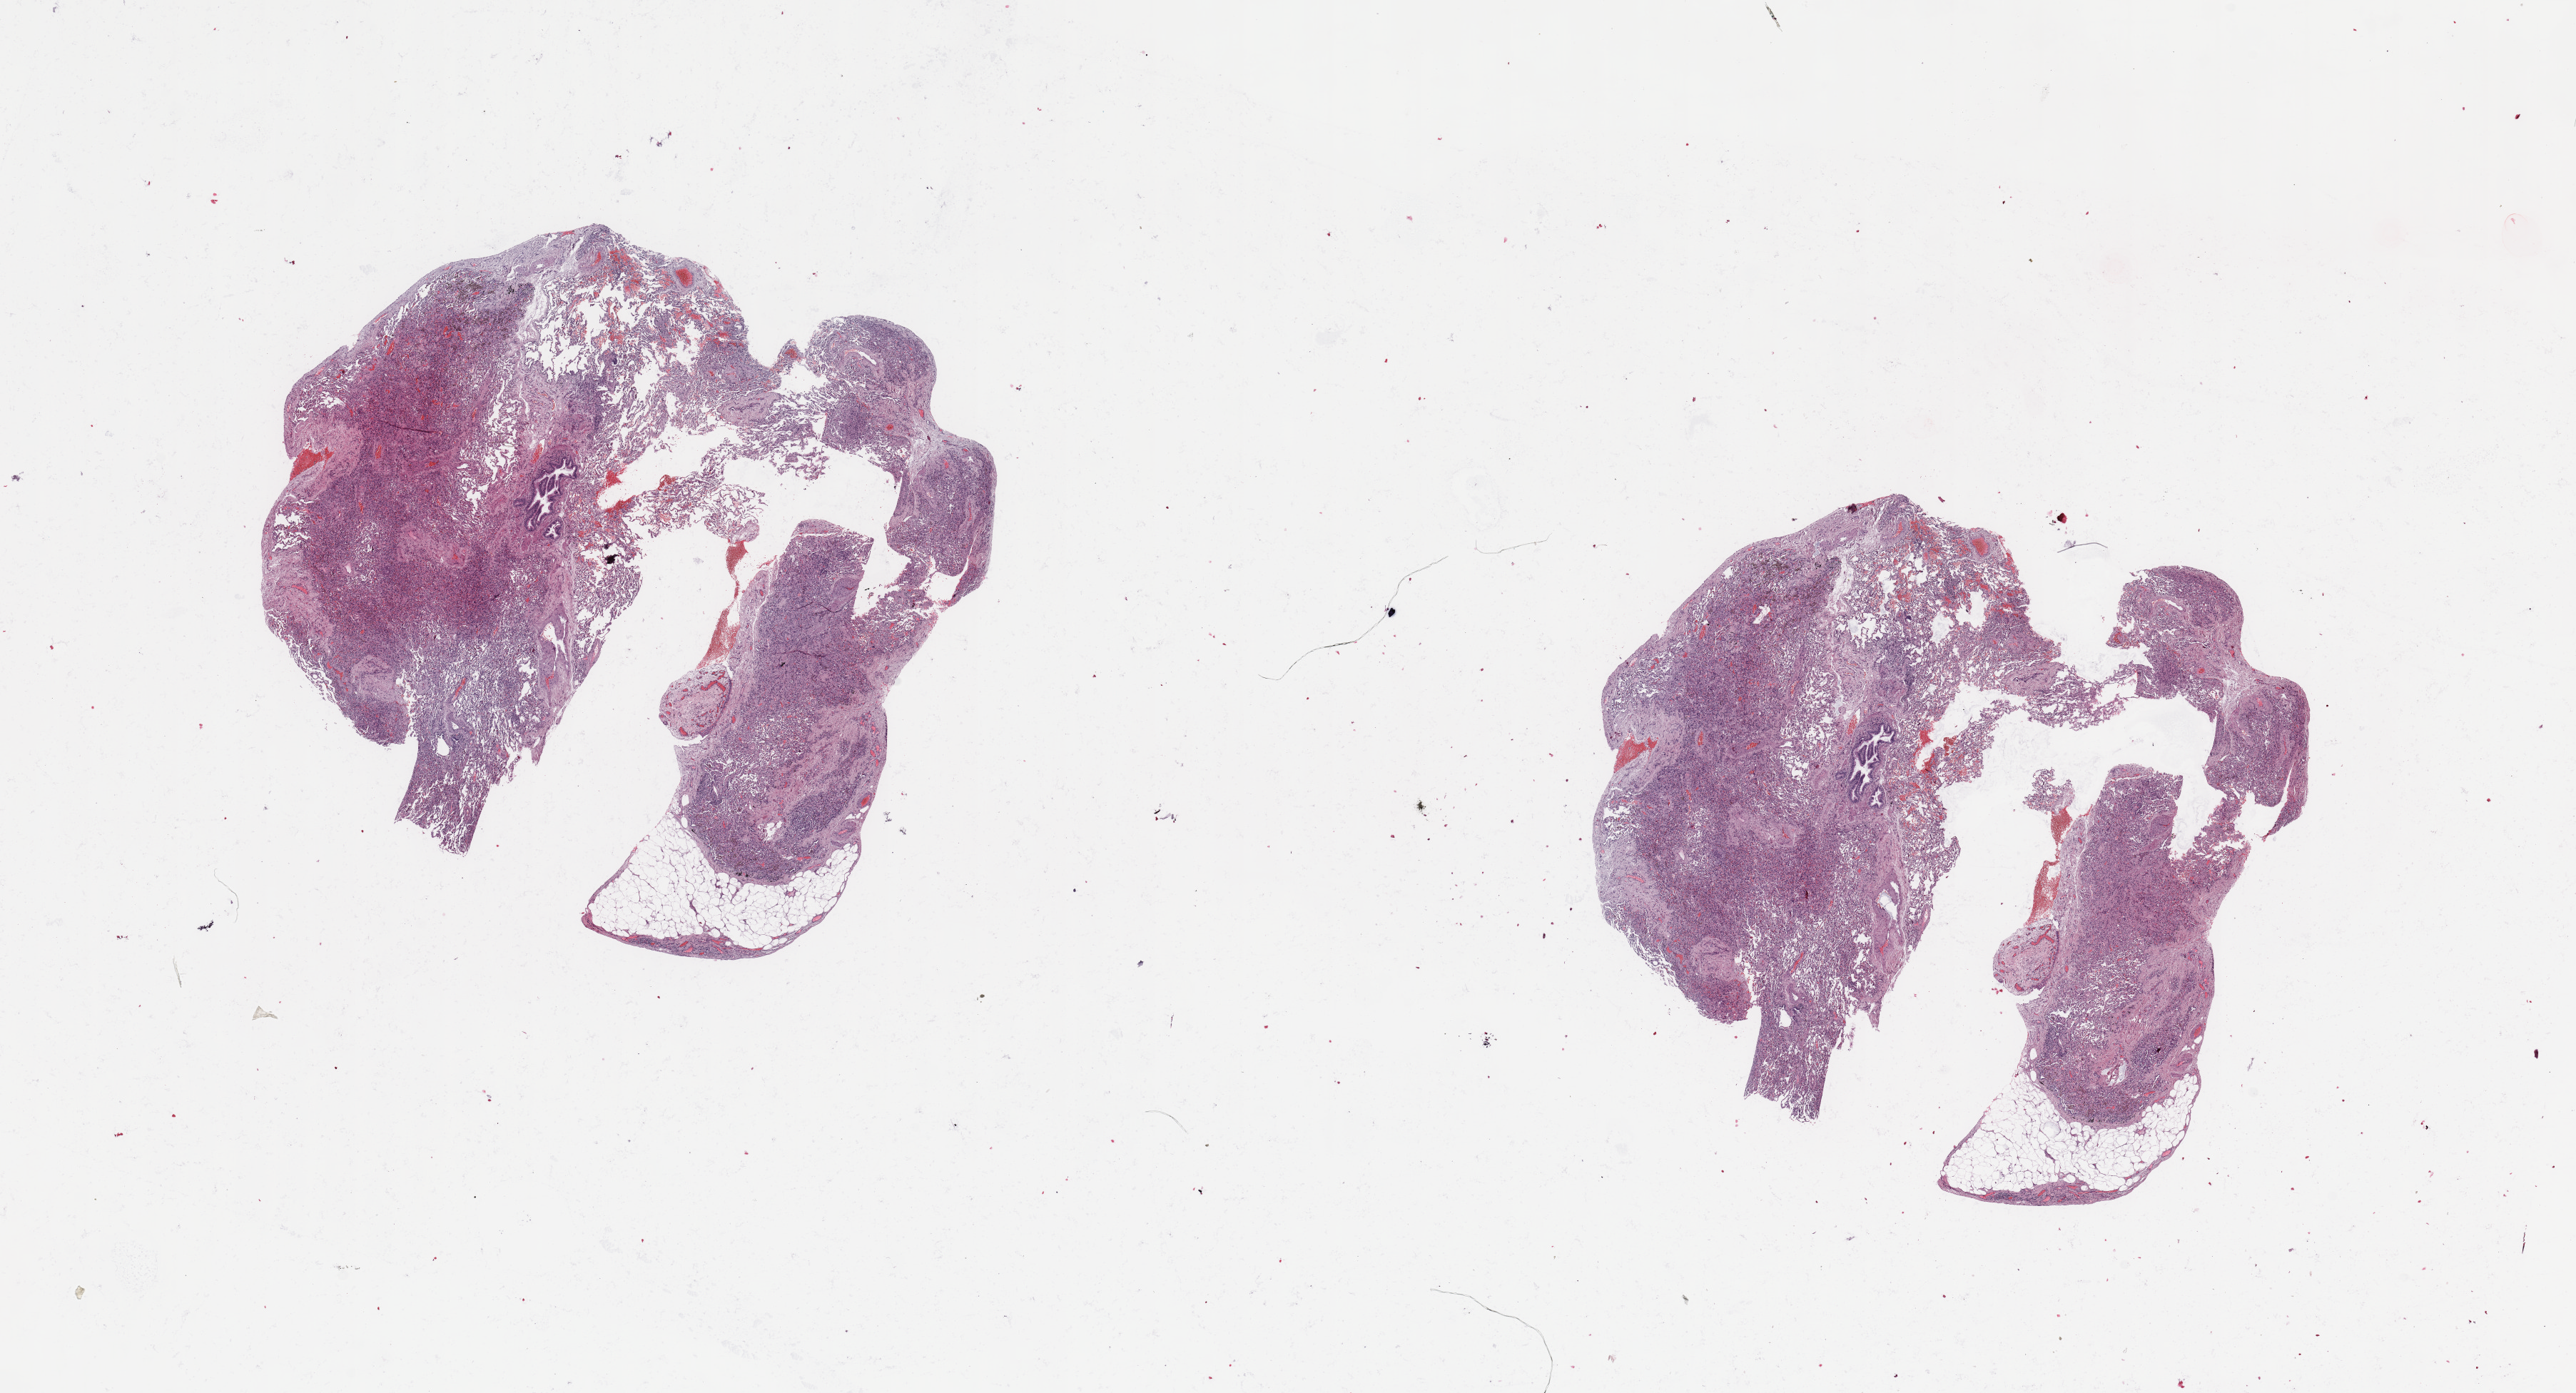
Whole-slide histology image, Hematoxylin and eosin (H&E) stained — shown as a low-resolution overview of the whole scanned area (about 28.5 x 15.4 mm); lung, normal (non-tumour) tissue. Male, 54 y/o.
This section: normal (non-tumour) tissue from the same patient. Patient diagnosis: Squamous cell carcinoma, NOS.